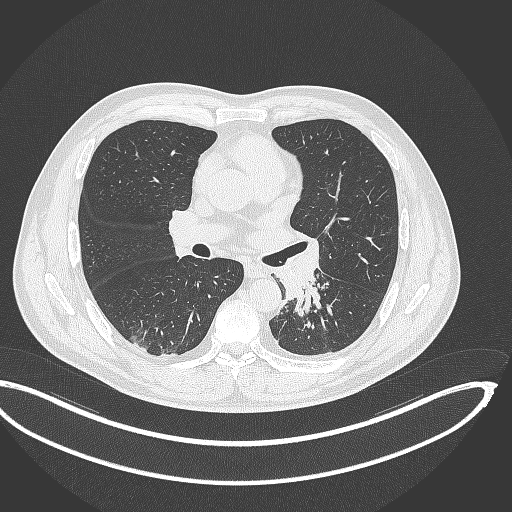
Chest CT, one axial slice. Position 197 of 362 along the scan axis. 120 kVp. Lung window (W 1500 / L -600 HU). 1 mm slice thickness. 512 × 512 image matrix. Male patient, age 50 years. Case-level facts recorded for this patient, not image findings: clinical TNM (as recorded): T2a N3 M0.
Annotated regions visible in this slice (rectangle marked by the reading radiologist):
- lung tumour (recorded histology: squamous cell carcinoma): box from (x=279, y=272) to (x=325, y=316) px